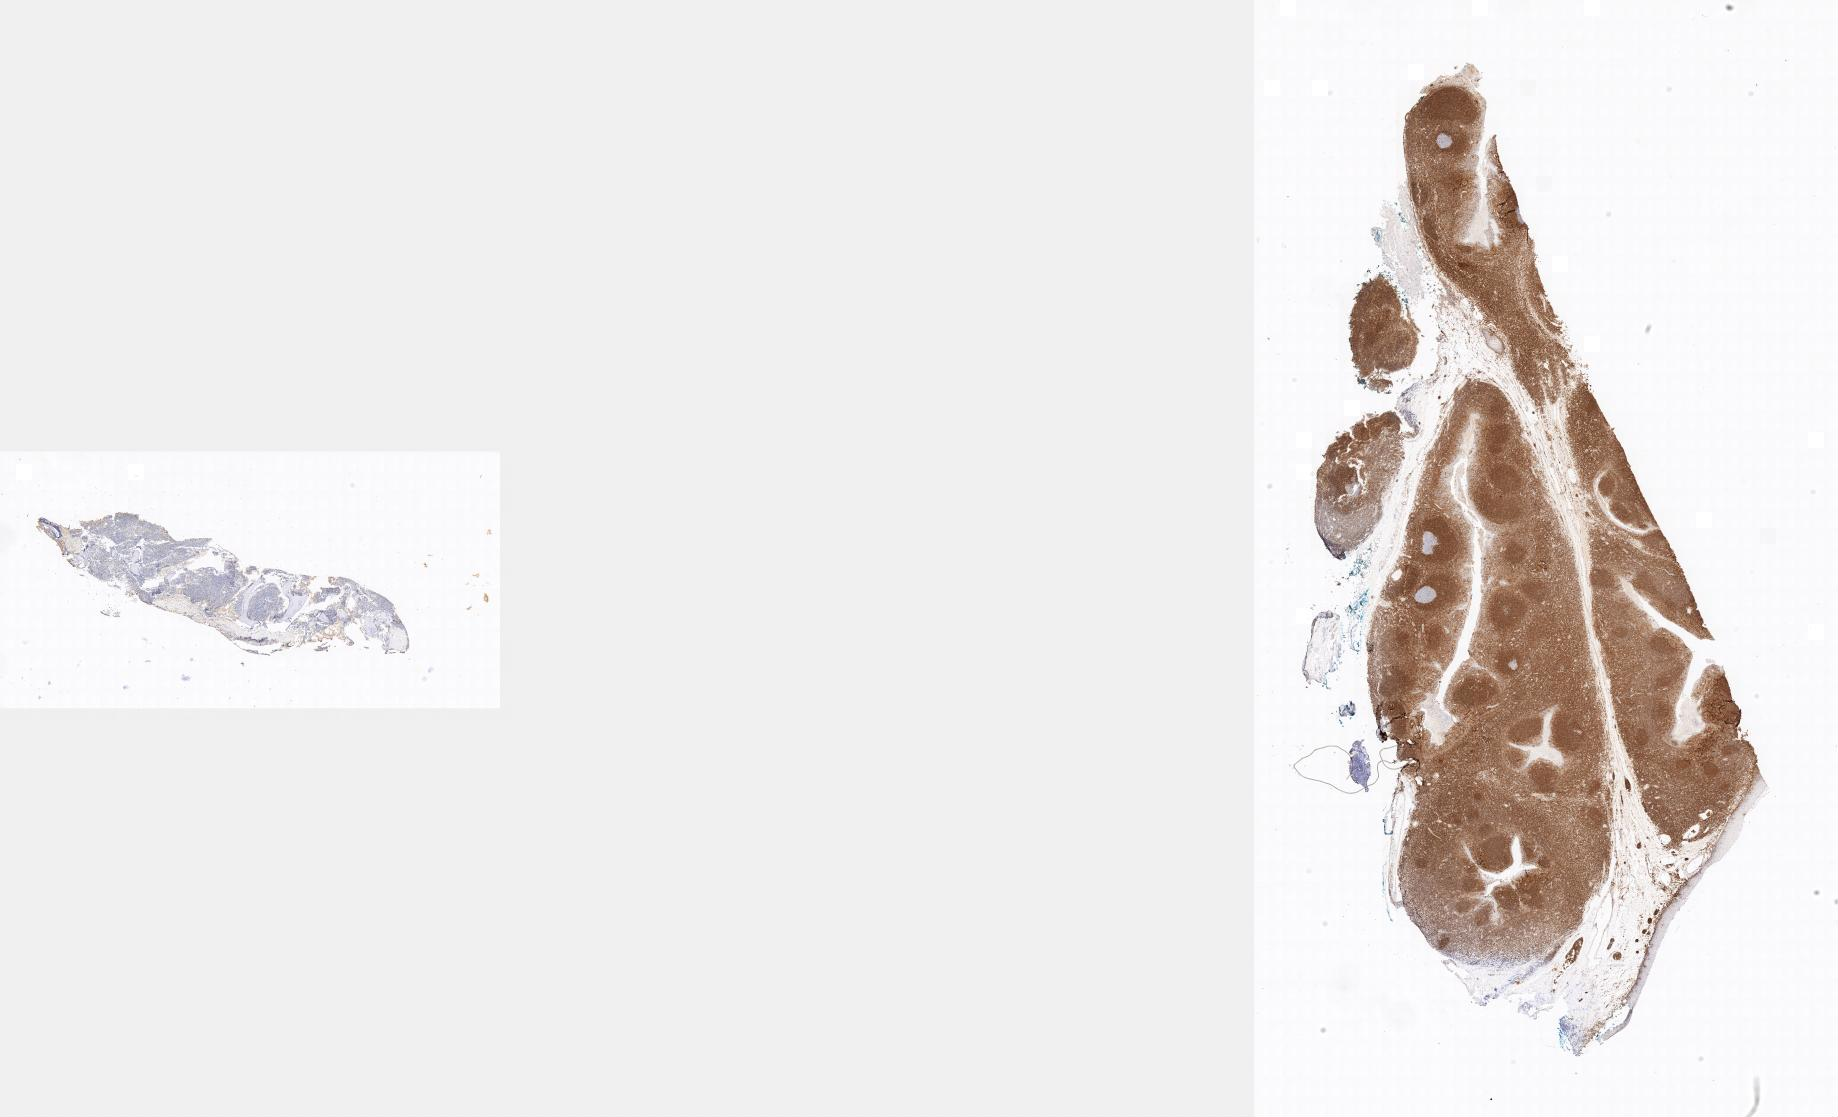
Immunohistochemistry (IHC) whole-slide image stained for BCL2, low-resolution overview of the scanned area; specimen: tumor tissue; site: bone marrow. Patient: female, age at initial diagnosis 3 years.
Histologic diagnosis: Burkitt lymphoma, NOS.